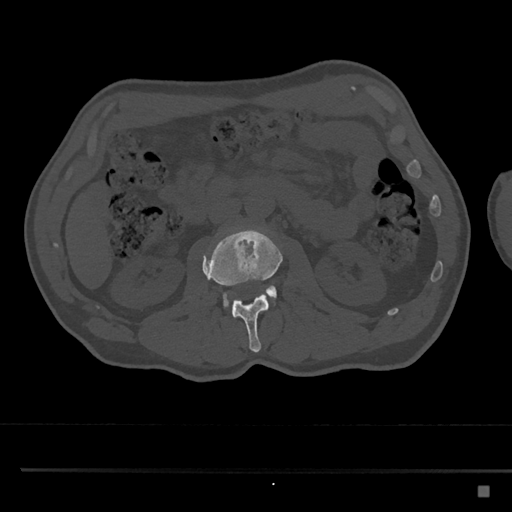
CT including the spine, one axial slice; slice 742 of 797 in the series (ordered by position); 120 kVp; bone window (W 1800 / L 400 HU); 512 × 512 image matrix, field of view 391 × 391 mm. Male patient, age 59 years. Case-level facts recorded for this patient, not image findings: primary cancer: prostate.
Outlined on this slice (semi-automatically segmented with operator editing):
- L2 vertebra: bounding box (x1, y1, x2, y2) in pixels: (202, 227, 283, 353)
- L3 vertebra: (222, 285, 277, 309)